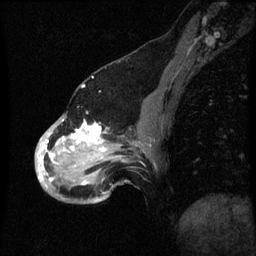
Breast MRI (dynamic contrast-enhanced), one sagittal slice; position 21 of 60 along the scan axis; dynamic contrast-enhanced series, image 2 of 3 at this slice position (ordered by acquisition); 1.5 T; TE 4.2 ms, TR 8.9 ms; 2 mm slice thickness; 256 × 256 image matrix. Female patient, age 49 years. From the clinical record (not read from this slice): setting: breast cancer imaged before/during neoadjuvant chemotherapy; receptor status: HR-positive, HER2-negative.
Annotated regions visible in this slice (semi-automatic segmentation, software-assisted and operator-edited):
- analysis volume of interest (the breast-tissue region the enhancement analysis was run in; not a lesion): bounding box <36,114,145,199> (left, top, right, bottom; pixels)
- tumour enhancement mask (voxels above the 70 % enhancement threshold inside the analysis volume of interest): <38,122,107,181>